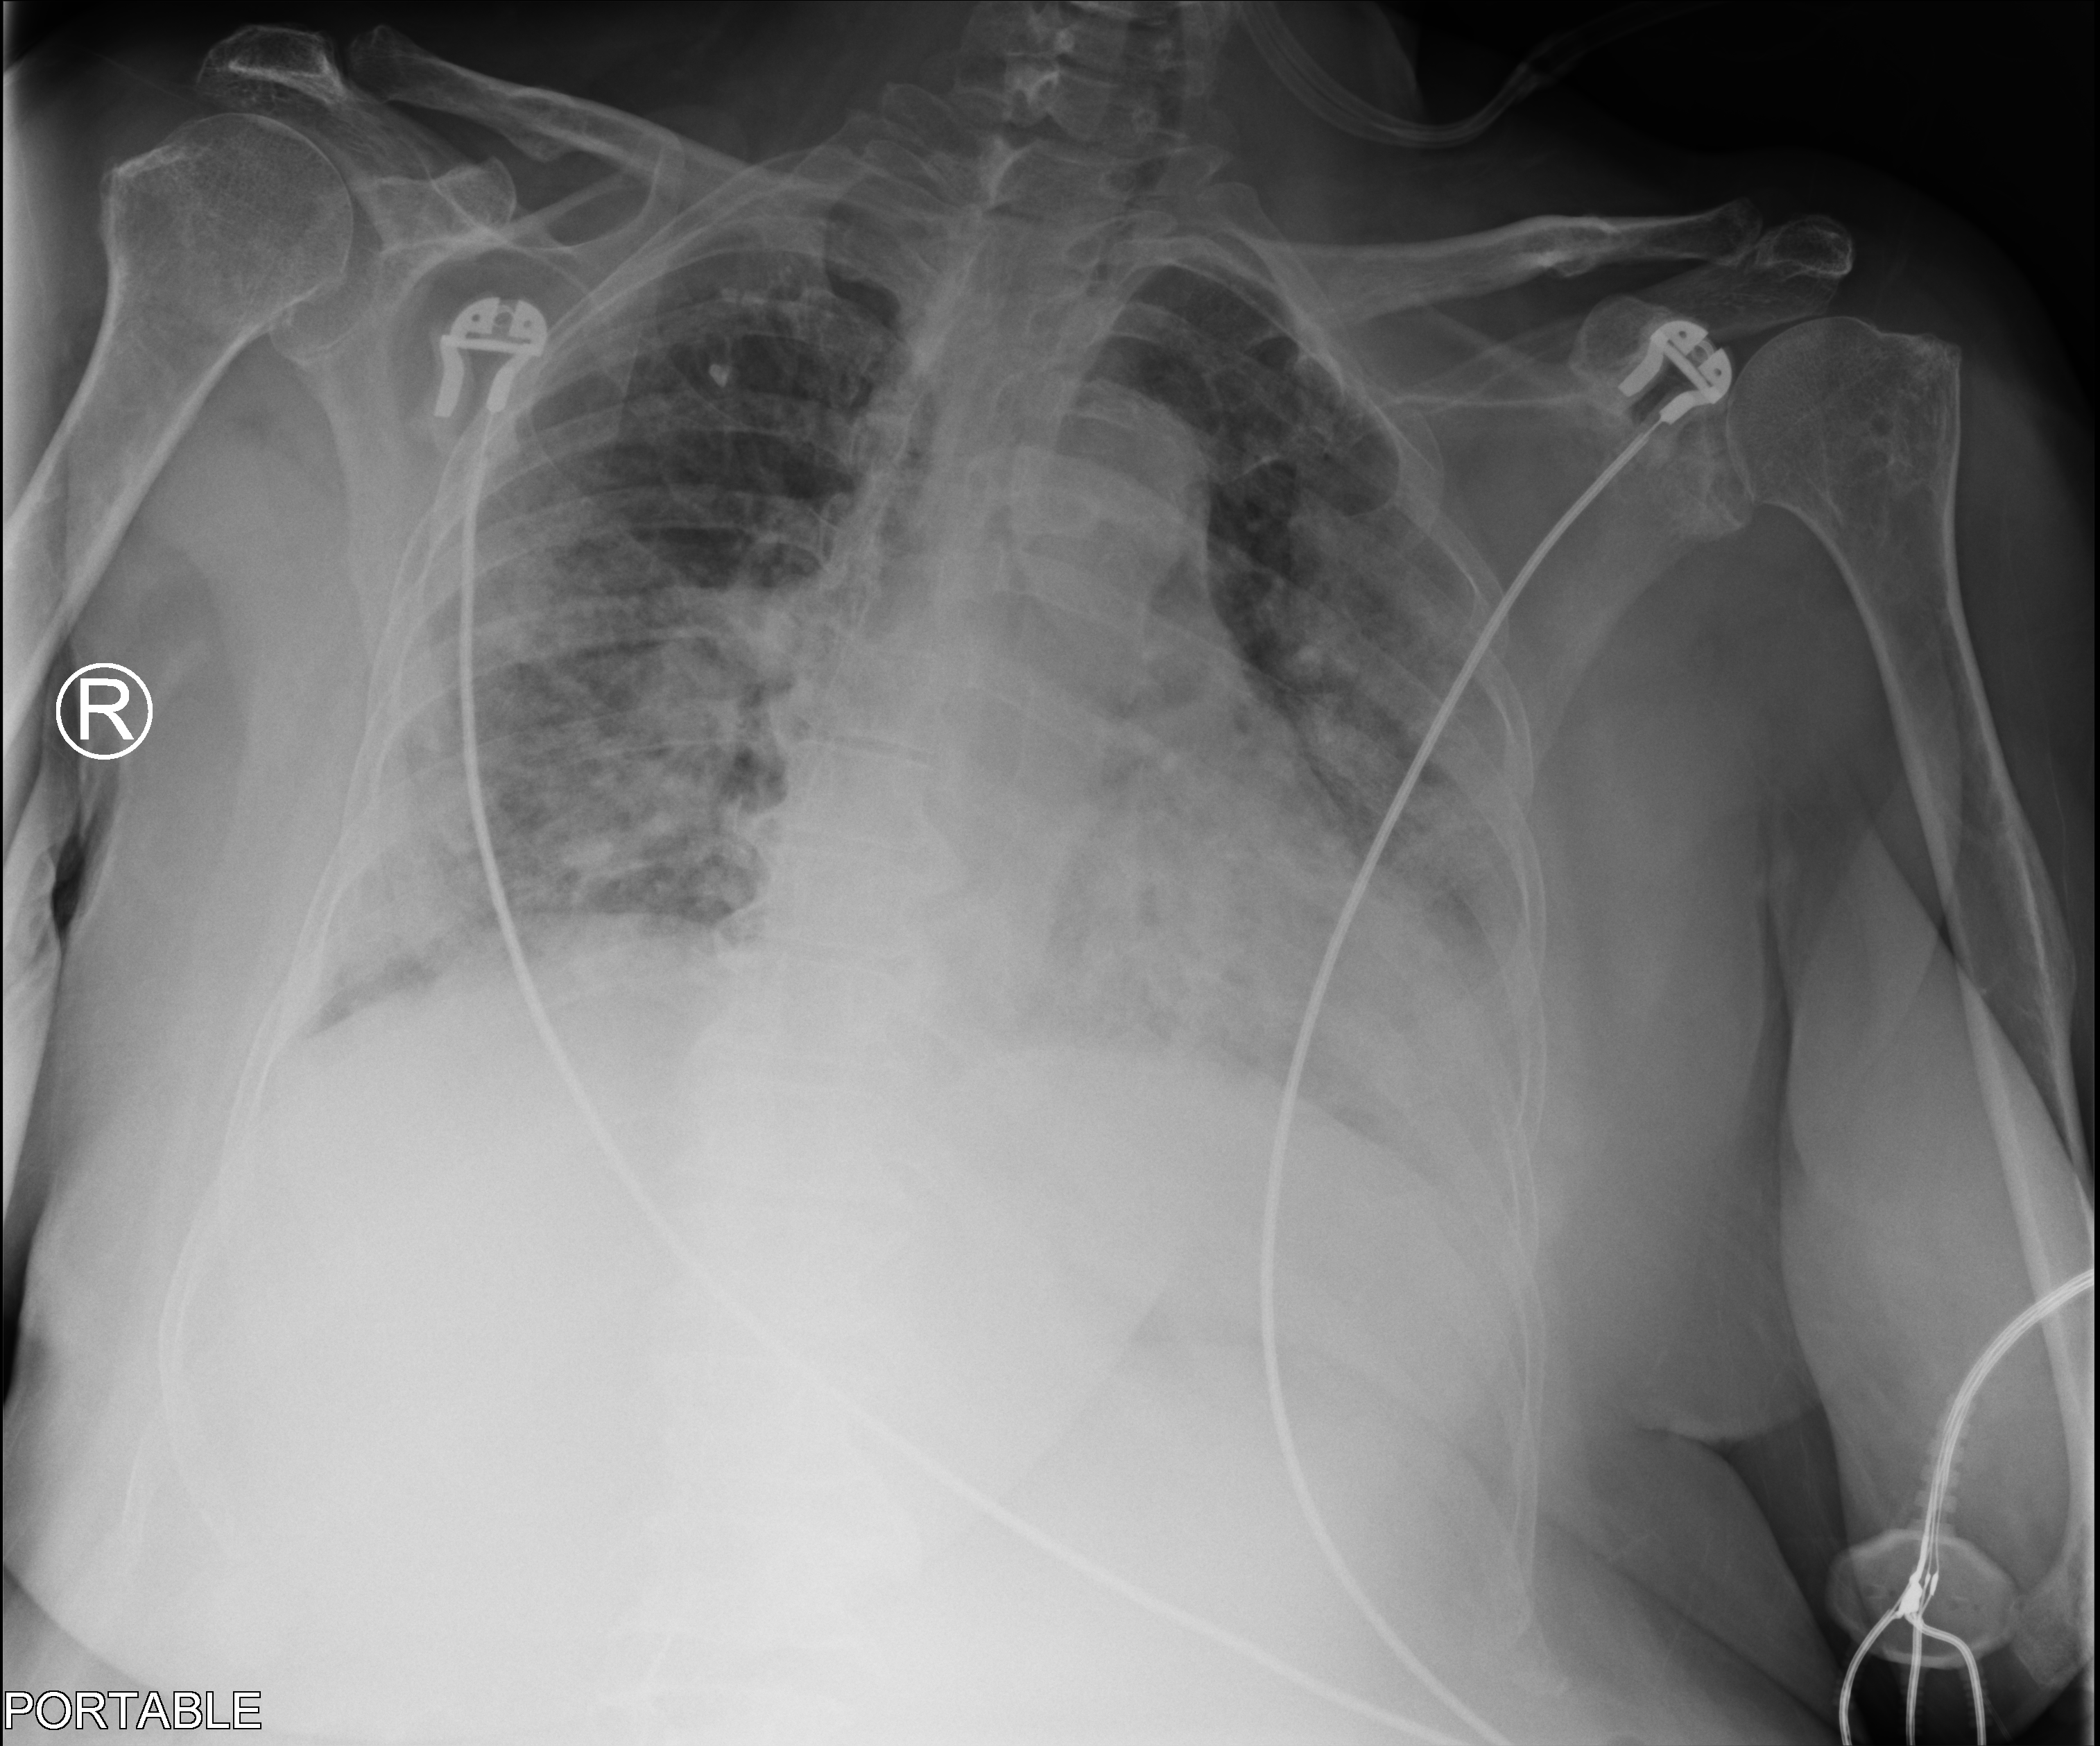
Chest X-ray (portable), anteroposterior (AP) projection. Patient hospitalised with COVID-19; female, aged 75–90 years.
Admission-level facts for this patient (not findings on this image; timing relative to this image not recorded): length of hospital stay: 37 days.